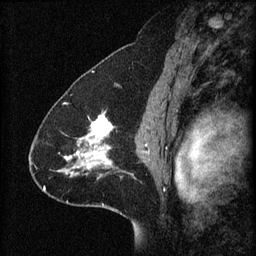
Breast MRI (dynamic contrast-enhanced), one sagittal slice. Position 42 of 60 along the scan axis. 3 images stored at this slice position (order not interpretable as contrast timing). 1.5 T. TE 4.2 ms, TR 8.2 ms. 256 × 256 image matrix, field of view 200 × 200 mm. Female patient, age 41 years.
Annotated regions visible in this slice (semi-automatically segmented with operator editing):
- analysis volume of interest (the breast-tissue region the enhancement analysis was run in; not a lesion): bounding box (x1, y1, x2, y2) in pixels: (59, 112, 122, 179)
- tumour enhancement mask (voxels above the 70 % enhancement threshold inside the analysis volume of interest): (60, 114, 114, 175)